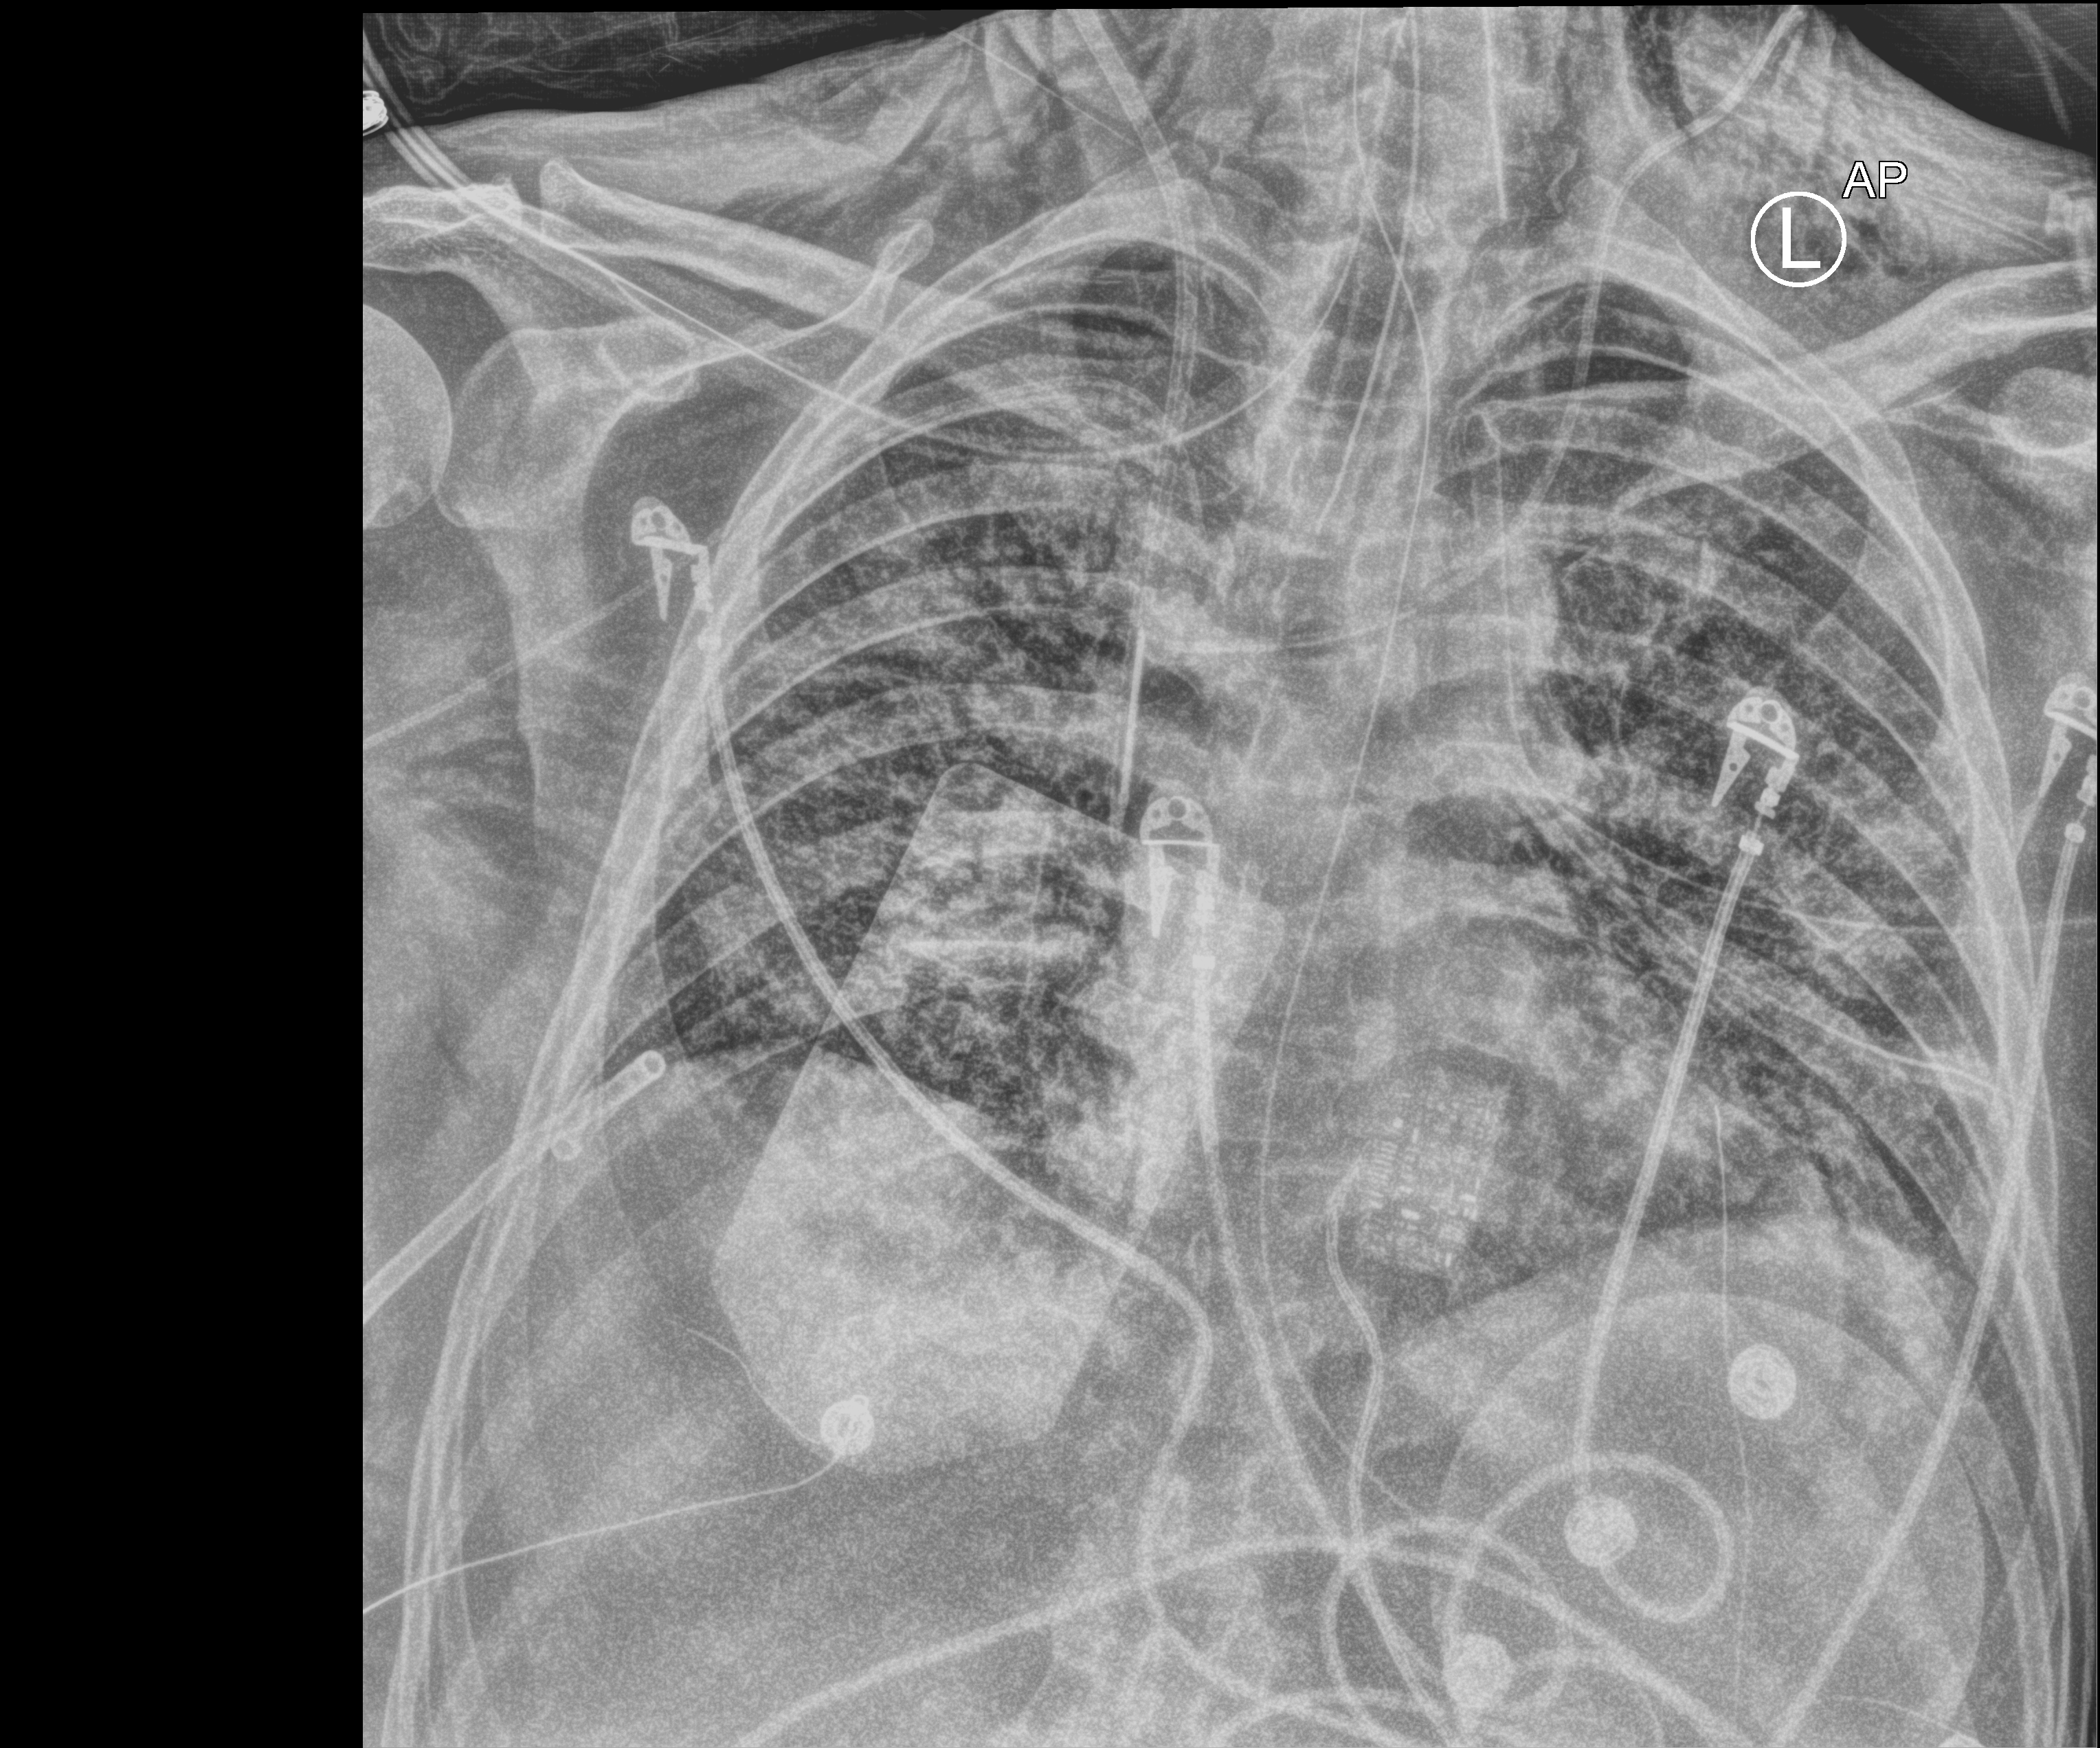
Bedside chest radiograph (computed radiography), anteroposterior (AP) projection. Patient hospitalised with COVID-19; male, aged 18–59 years.
Admission-level facts for this patient (not findings on this image; timing relative to this image not recorded):
- chronic kidney disease (admission record): no
- mechanically ventilated during this hospital stay: yes
- admitted to intensive care during this hospital stay: yes